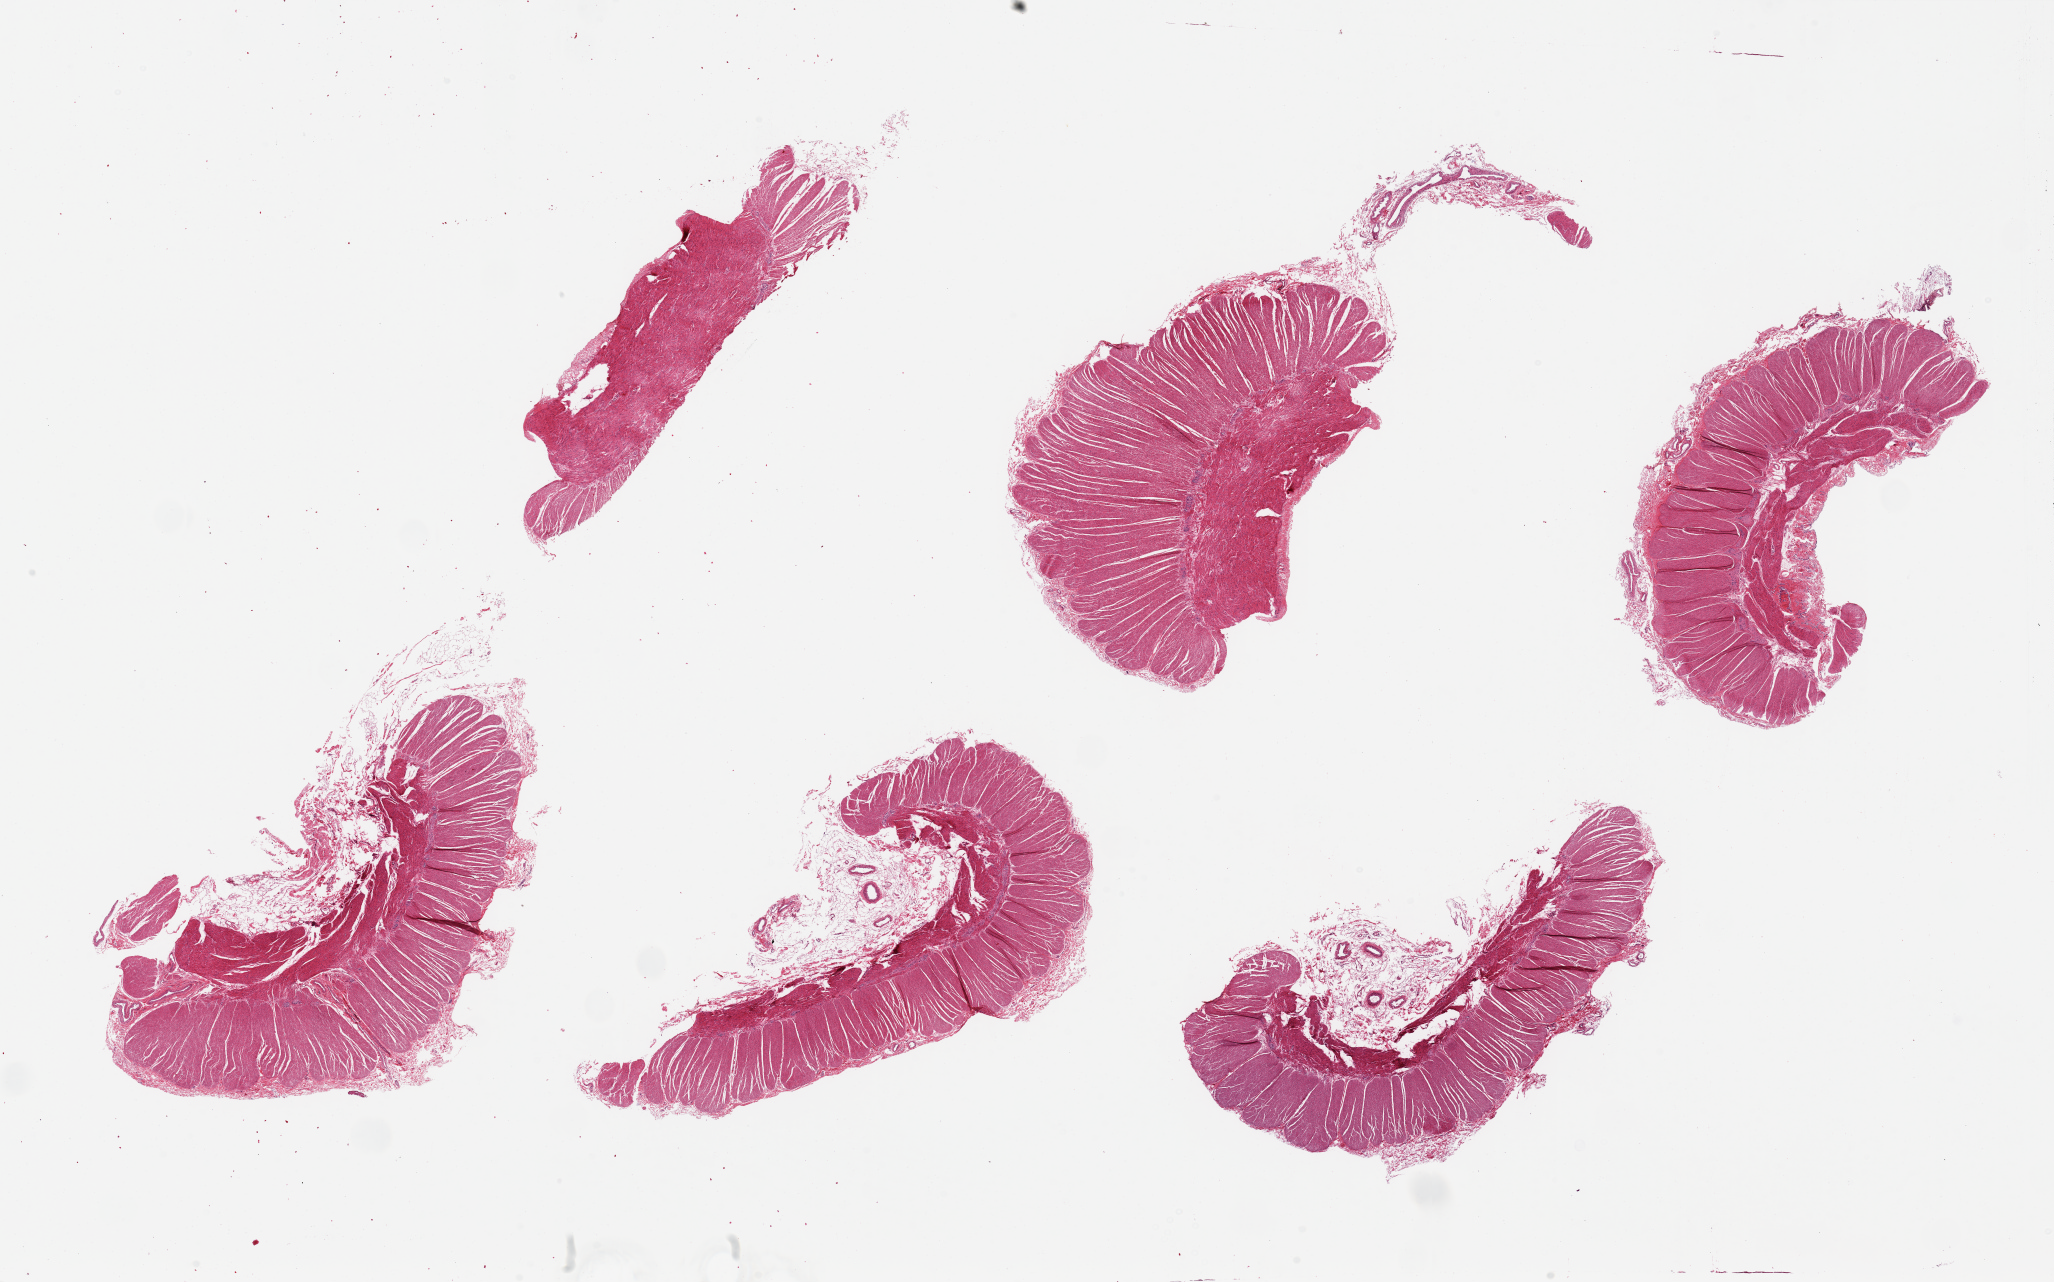
Whole-slide image, H&E stain — a low-resolution overview of the entire scanned area, about 32.5 x 20.3 mm, PAXgene-fixed, paraffin-embedded tissue, sampled site (target tissue): sigmoid colon, tissue donor sample. Donor: female.
Review note (as recorded): 6 pieces, up to 10x5mm; all muscle, good specimens.